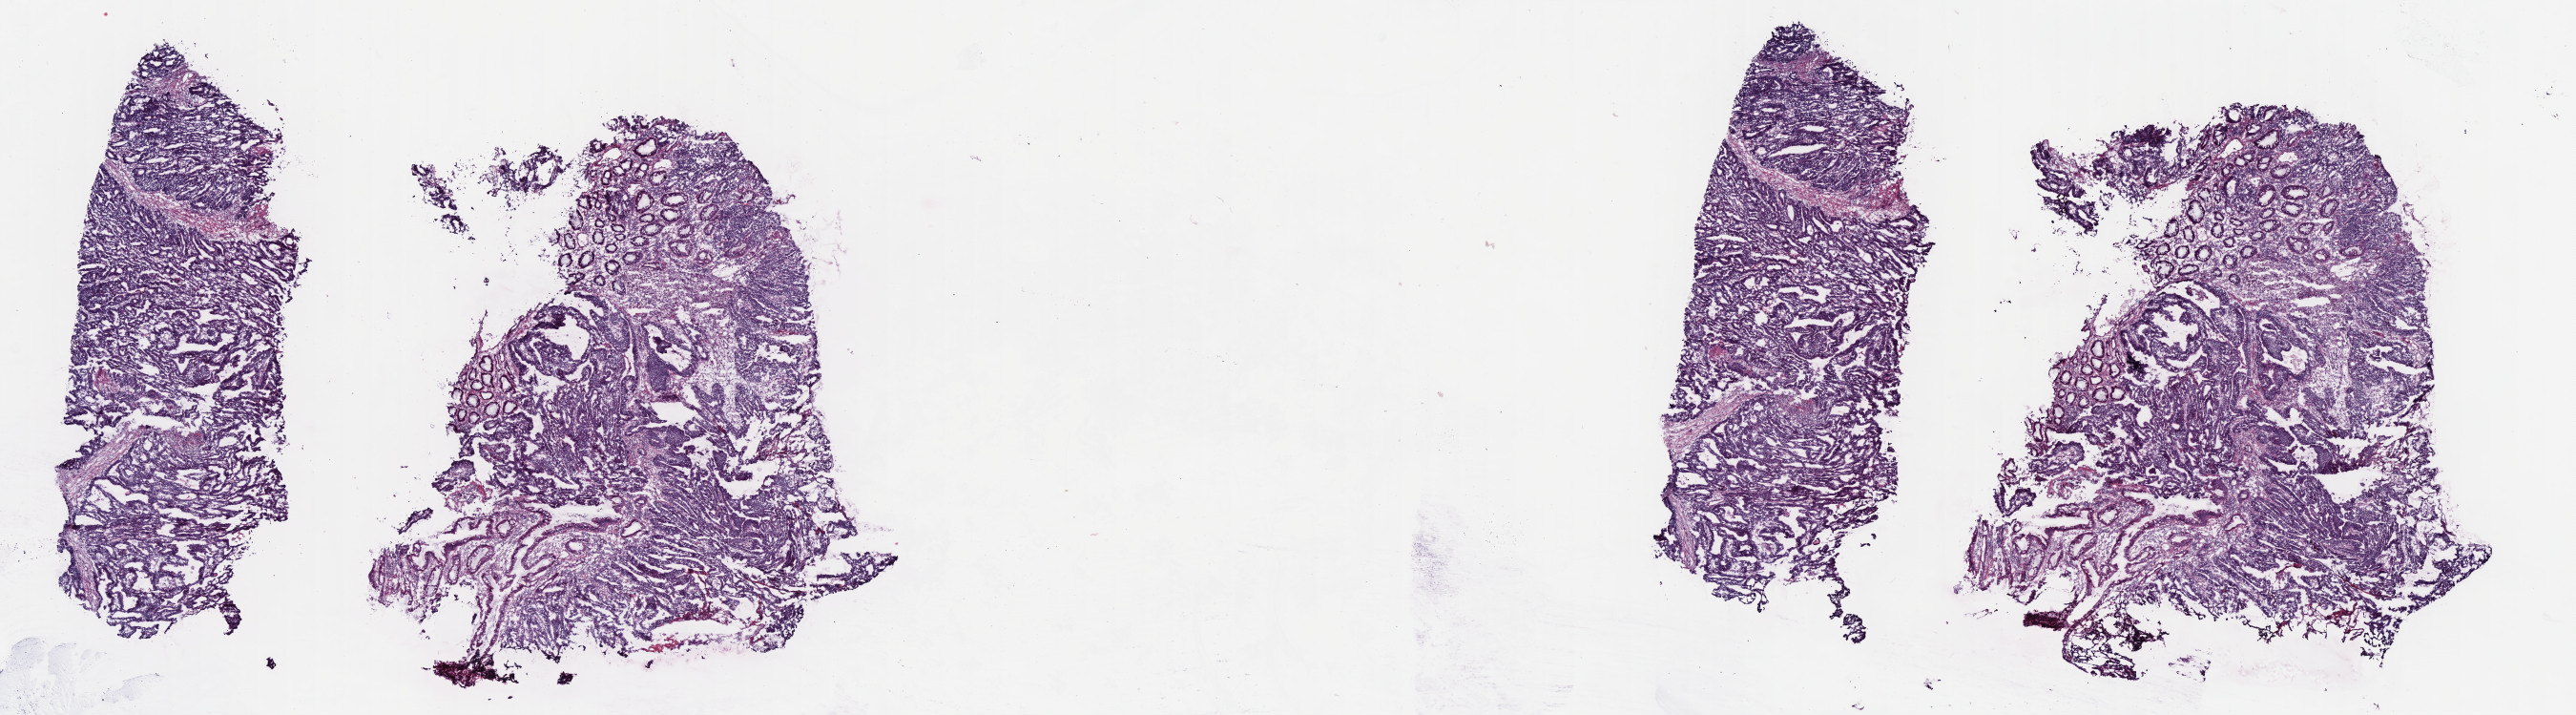
Whole-slide histology image, H&E-stained — low-resolution overview of the scanned area, about 21.6 x 6.0 mm; frozen section from the bottom of the tissue portion; rectum, primary tumour sample. Patient: male, age at initial diagnosis 66 years. Composition of this section per pathologist review: tumour cells 70%, tumour nuclei 75%, normal cells 10%, stromal cells 18%, necrosis 2%. Infiltration values recorded for this section: lymphocyte infiltration 4%, monocyte infiltration 2%, neutrophil infiltration 0%.
• lymph nodes positive (case pathology): 3 of 16 examined
• AJCC pathologic stage: IV
• pathologic diagnosis: Adenocarcinoma, NOS